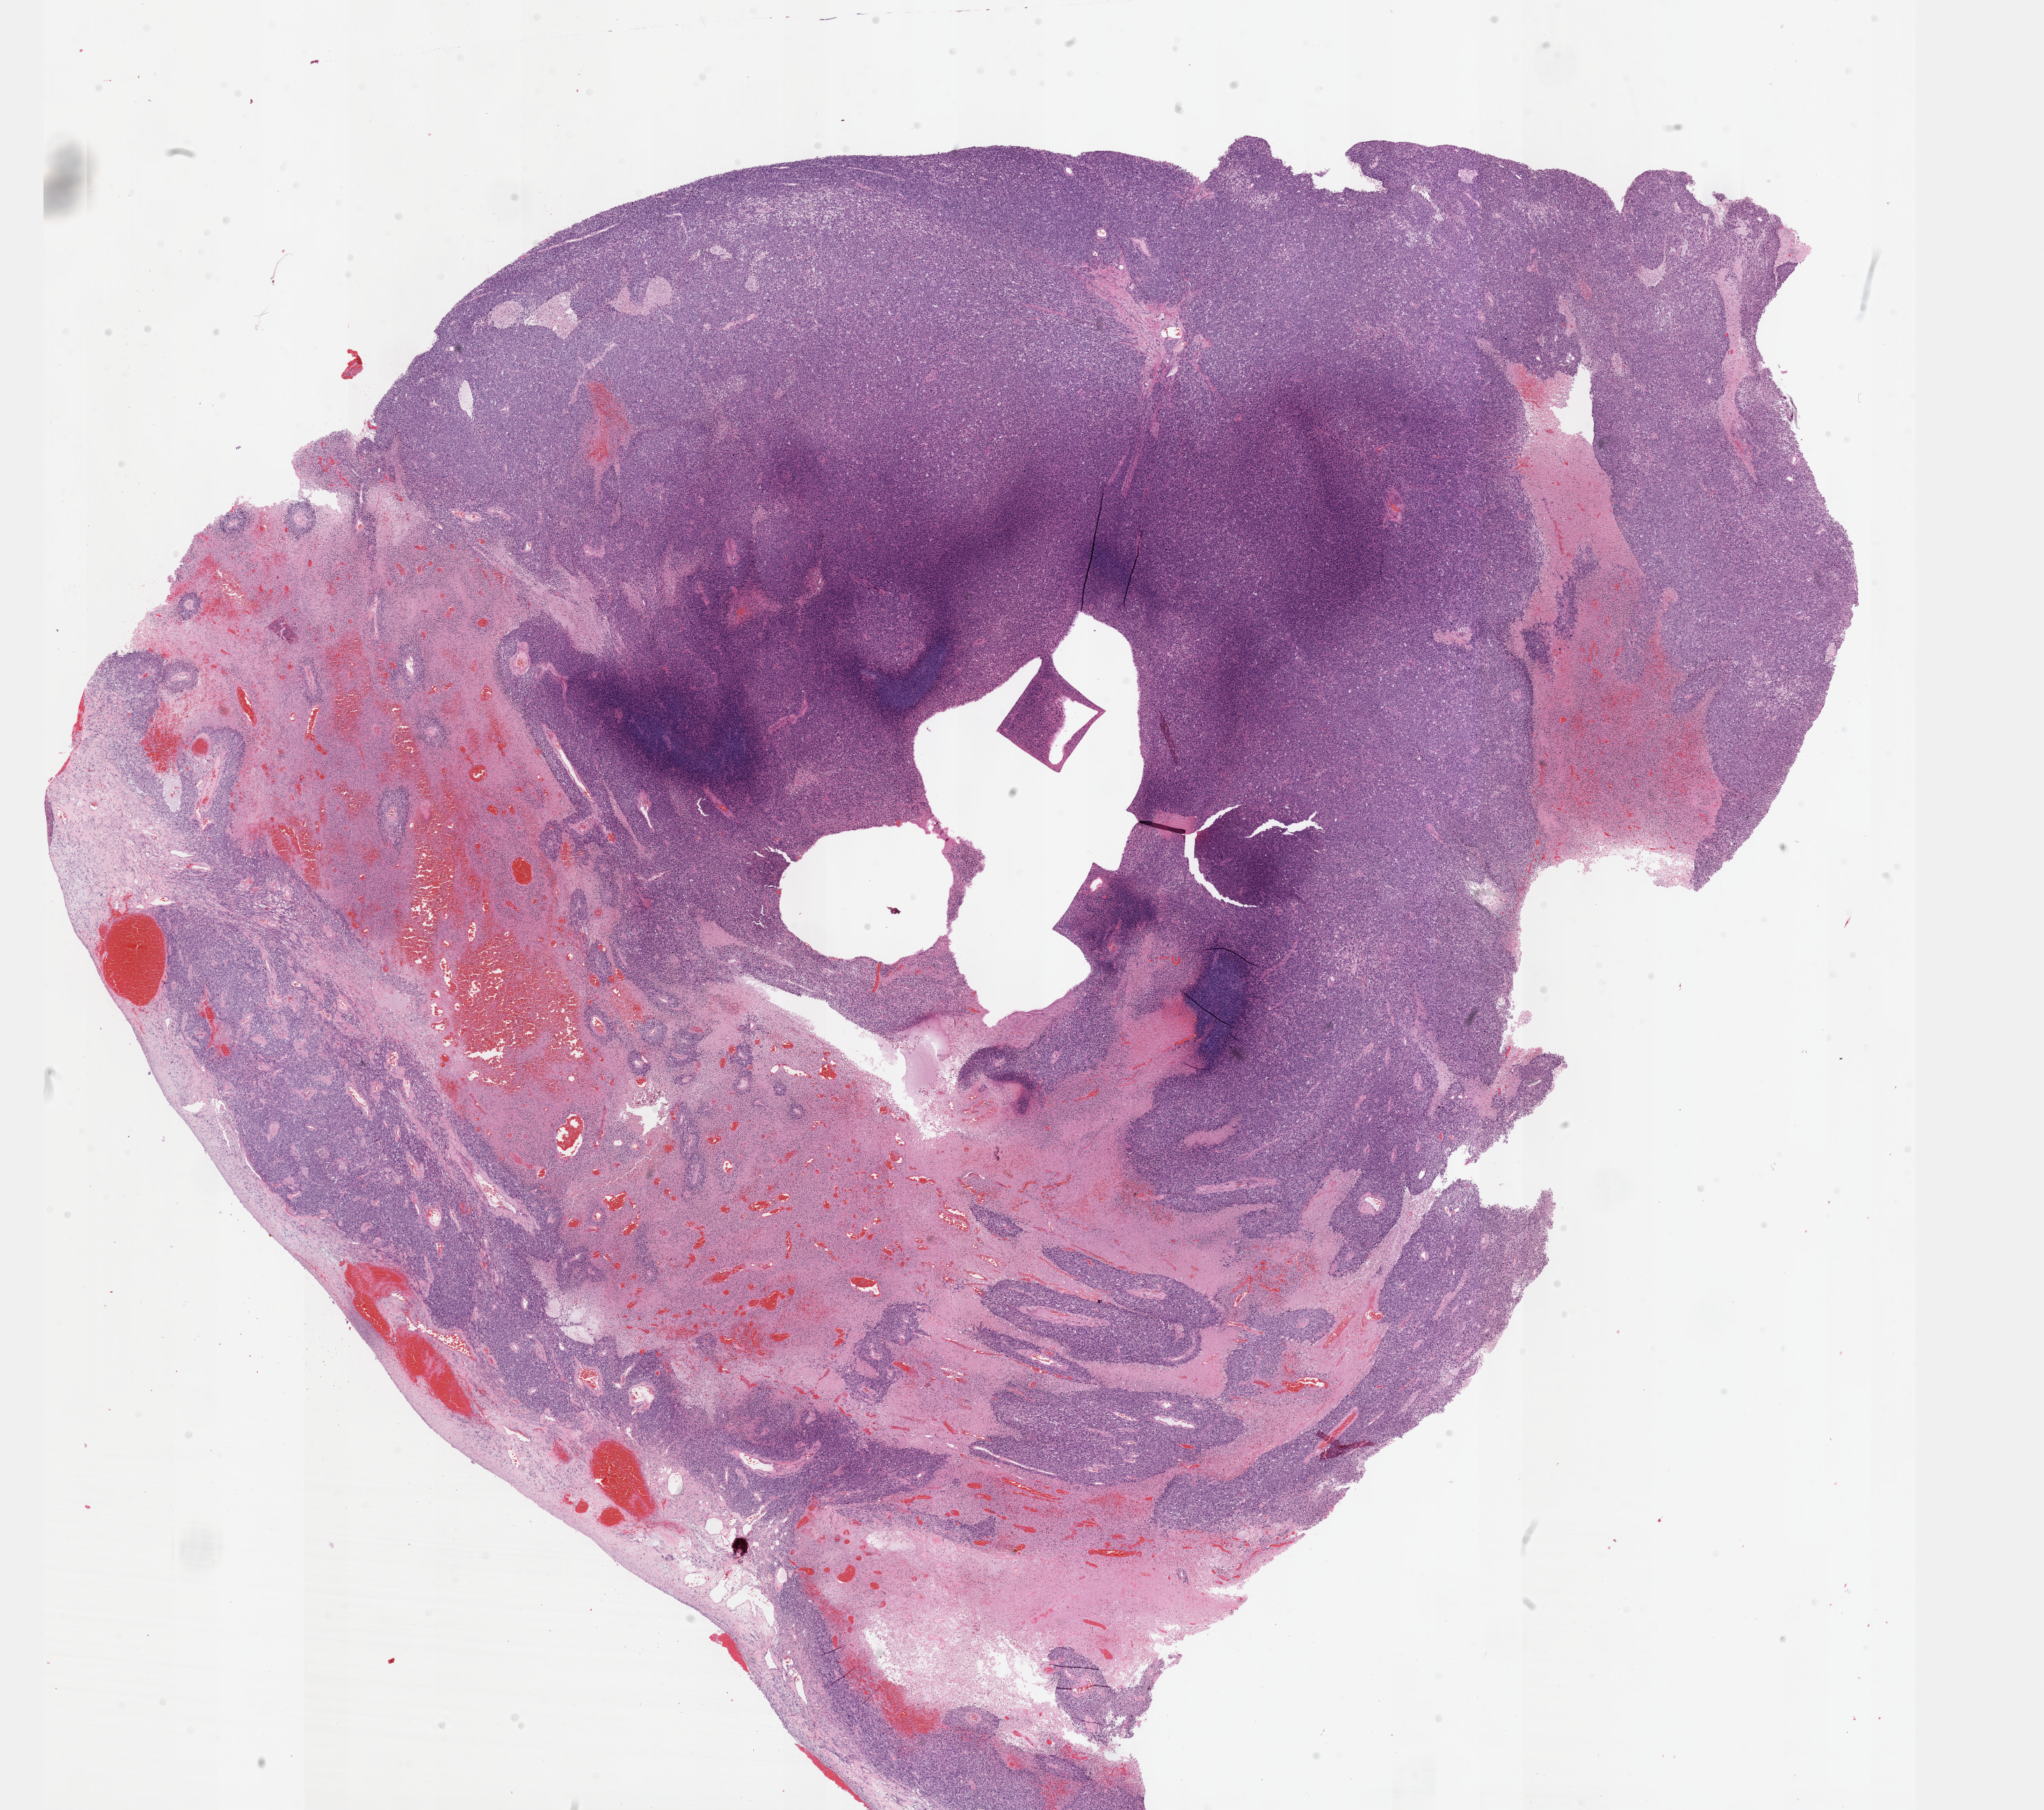
Hematoxylin and eosin (H&E) stained whole-slide image — low-resolution overview of the scanned area, about 23.6 x 20.9 mm (from a 40x scan). Formalin-fixed paraffin-embedded (FFPE) diagnostic section. Uterus, primary tumour sample. Female patient; age at initial diagnosis 58 years.
Pathologic diagnosis: Leiomyosarcoma, NOS.